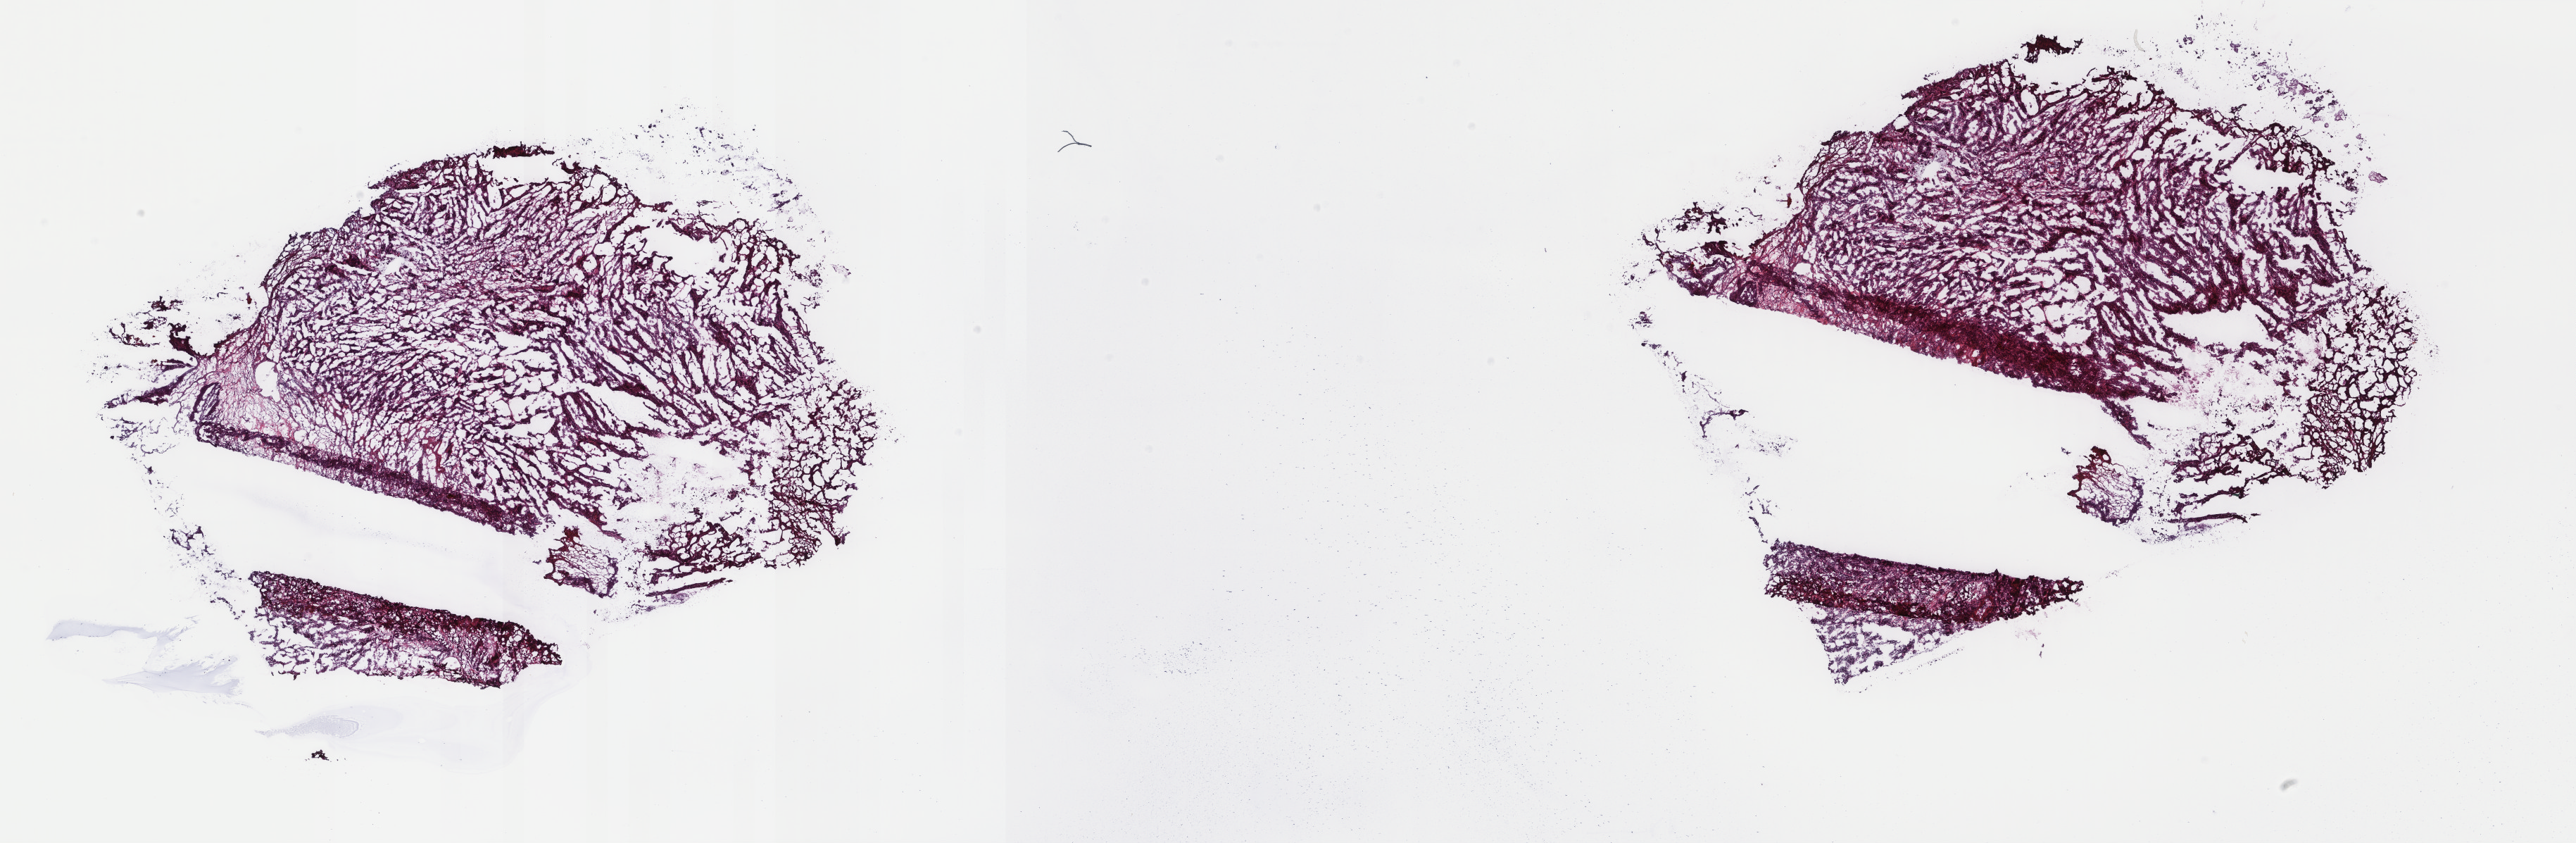
Whole-slide histology image, H&E-stained — whole scanned area (about 29.0 x 9.5 mm, acquisition: 40x scan) shown as a low-resolution overview, frozen section, primary tumour sample from the bladder. Patient: male, age at initial diagnosis 51 years. Histologic grade: high grade. Slide review estimates, as recorded: tumour cells 85%, tumour nuclei 85%, normal cells 0%, stromal cells 15%, necrosis 0%. Infiltration values recorded for this section: lymphocyte infiltration 2%, monocyte infiltration 1%, neutrophil infiltration 1%.
Histologic diagnosis: Transitional cell carcinoma. AJCC pathologic stage: II (6th edition).